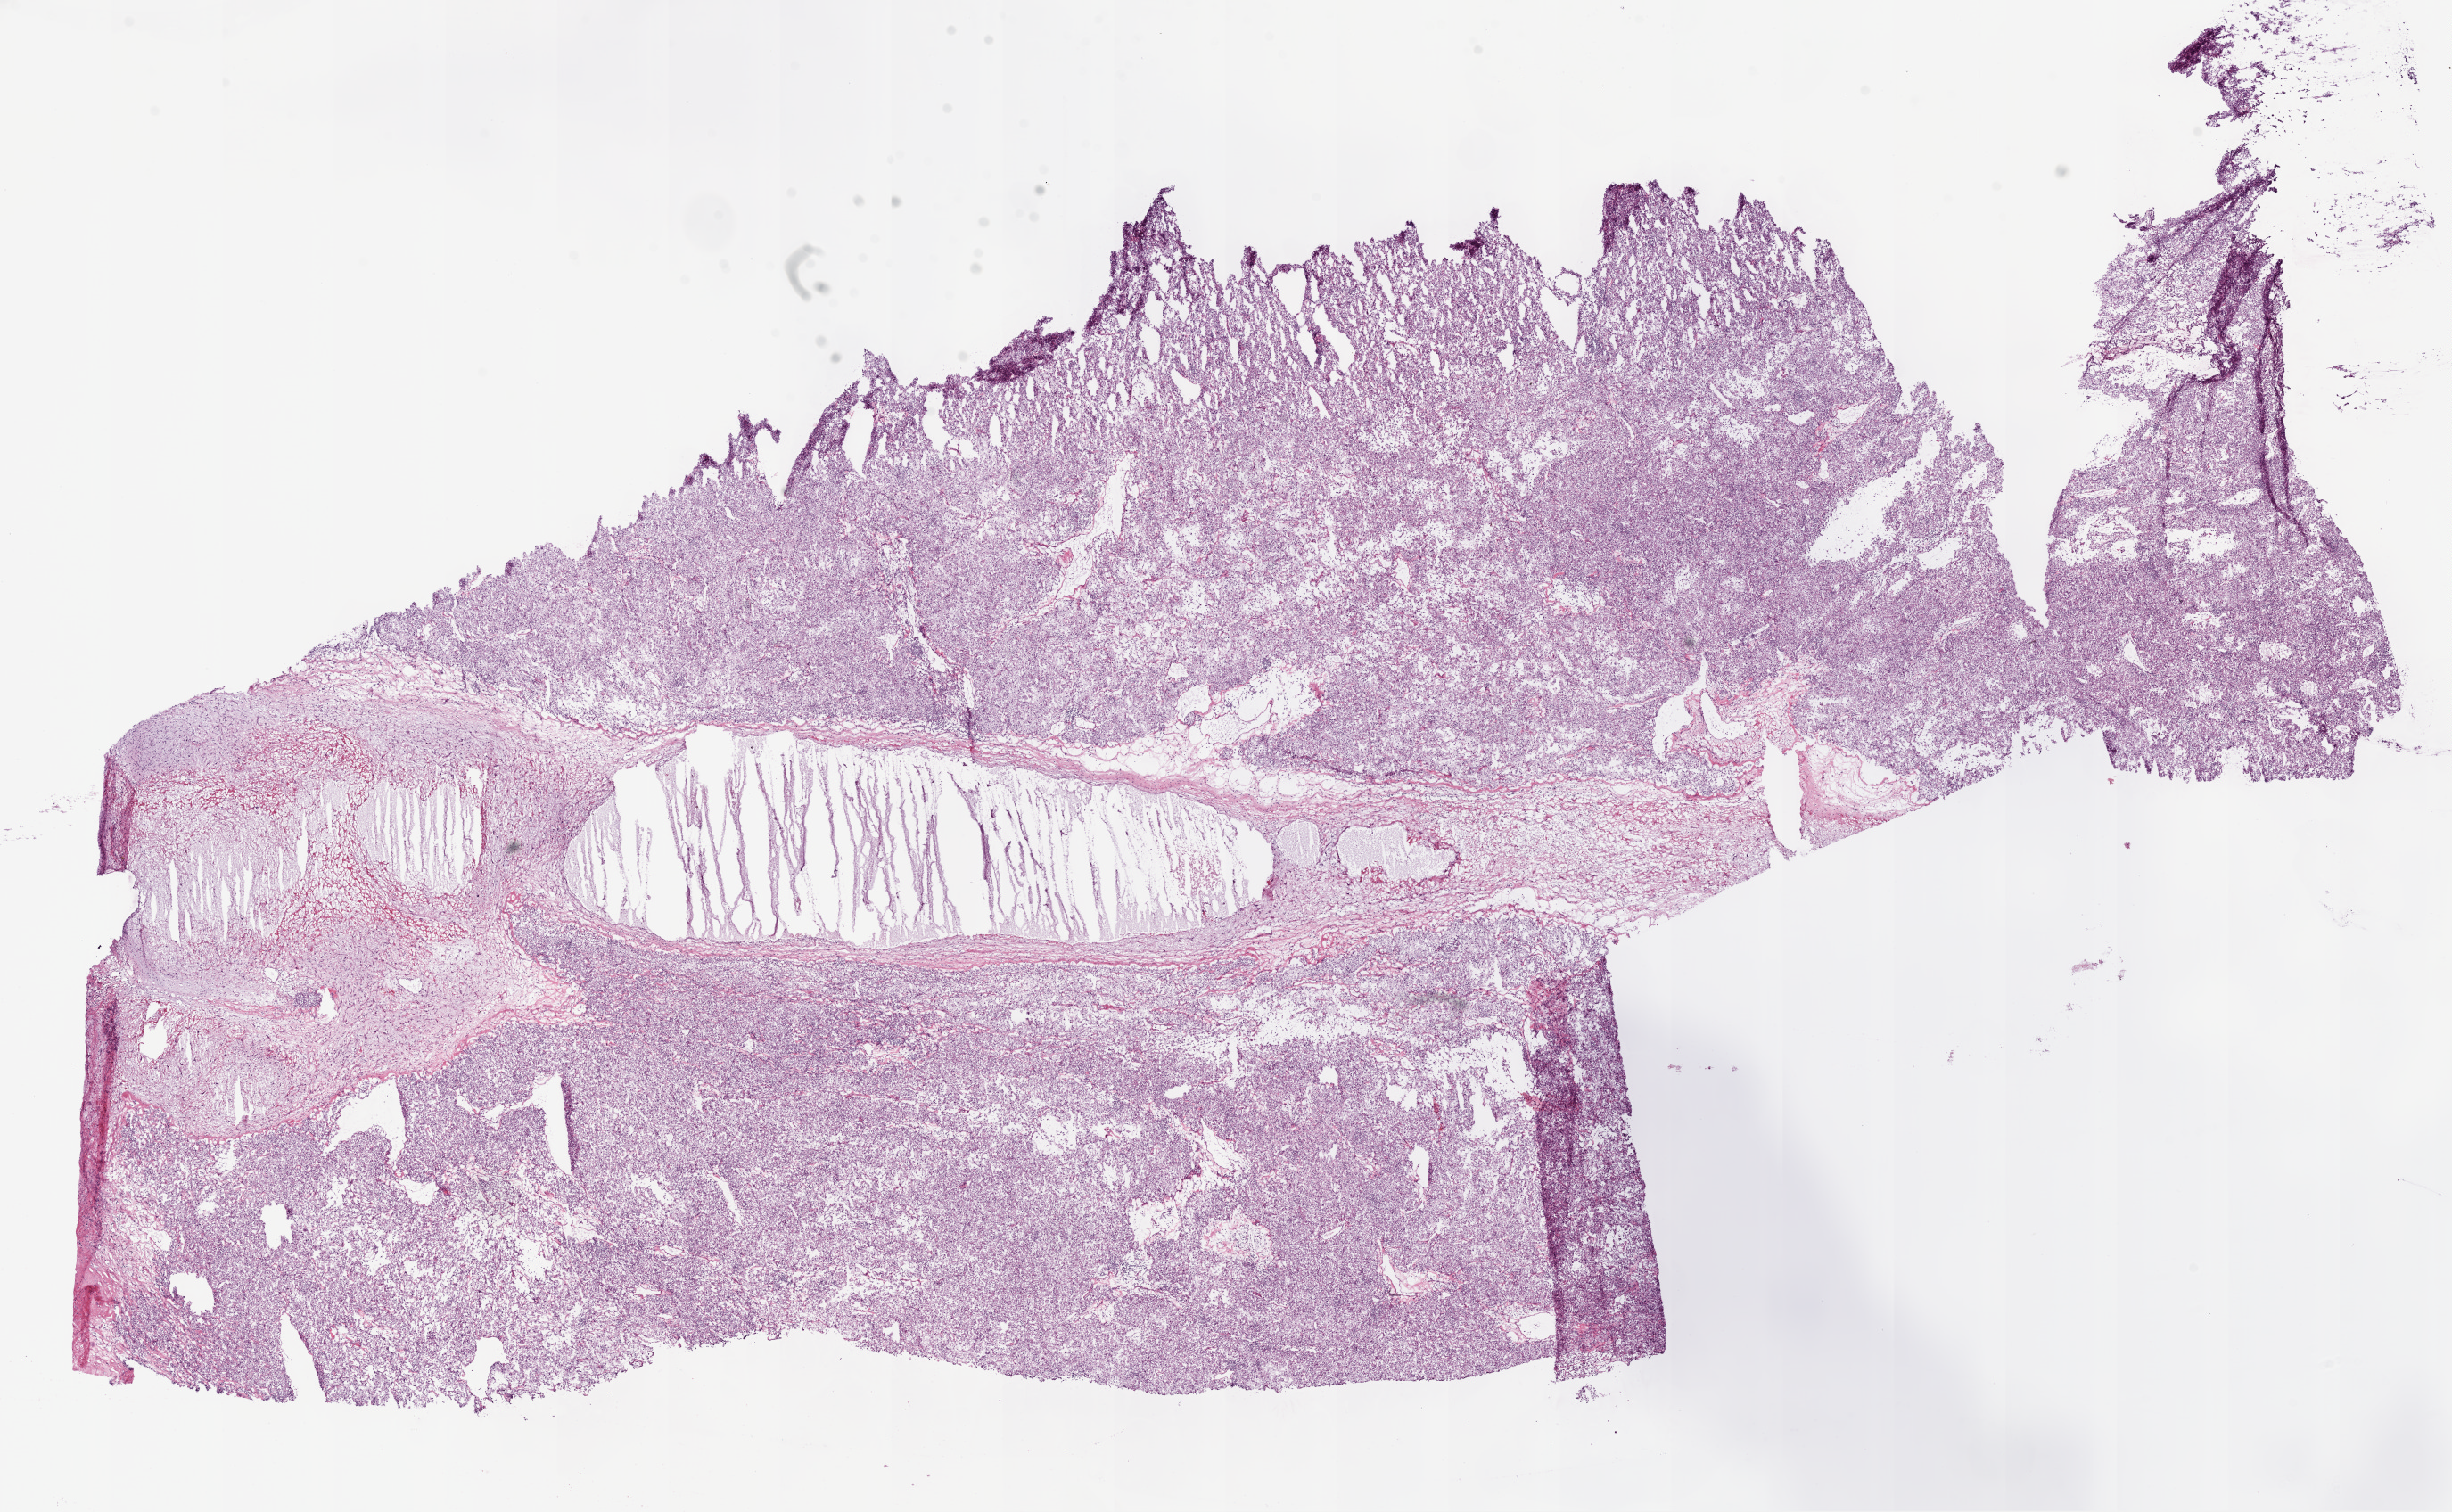
H&E-stained whole-slide image, whole scanned area (about 22.1 x 13.6 mm, slide scanned at 20x) shown as a low-resolution overview, frozen section from the bottom of the tissue portion, sample: primary tumour, kidney. Male patient; age at initial diagnosis 69 years. Histologic grade: G2 (moderately differentiated). Slide review estimates, as recorded: tumour cells 80%, tumour nuclei 85%, normal cells 0%, stromal cells 20%, necrosis 0%.
Lymph nodes positive (case pathology): 0 of 5 examined. AJCC pathologic stage: II. Histologic diagnosis: Clear cell adenocarcinoma, NOS.